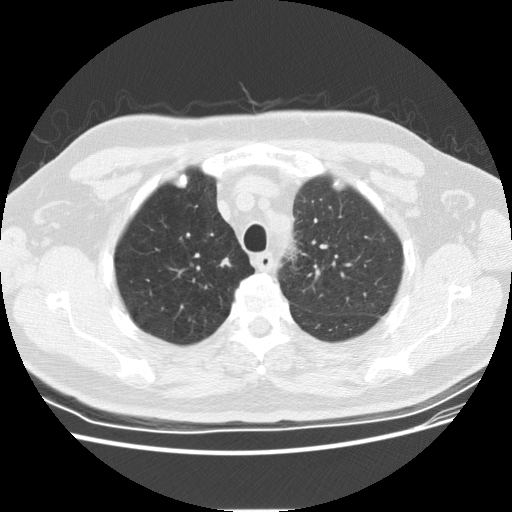
Chest CT (low-dose screening protocol), one axial image, second annual screen, lung window (W 1500 / L -600 HU), 2.5 mm slice thickness, standard (soft-tissue) reconstruction kernel (STANDARD), 512 × 512 image matrix. Male participant, aged 69 years at enrolment. Current smoker at enrolment.
- Lesion marked by an expert reader, box from (x=209, y=250) to (x=241, y=280) px.
- Reader record for this screening exam (exam-level; its link to the box is not recorded): non-calcified nodule or mass ≥4 mm, right lower lobe, 4 × 4 mm, smooth margins, soft tissue attenuation, pre-existing on the prior screen: yes; interval growth: no.